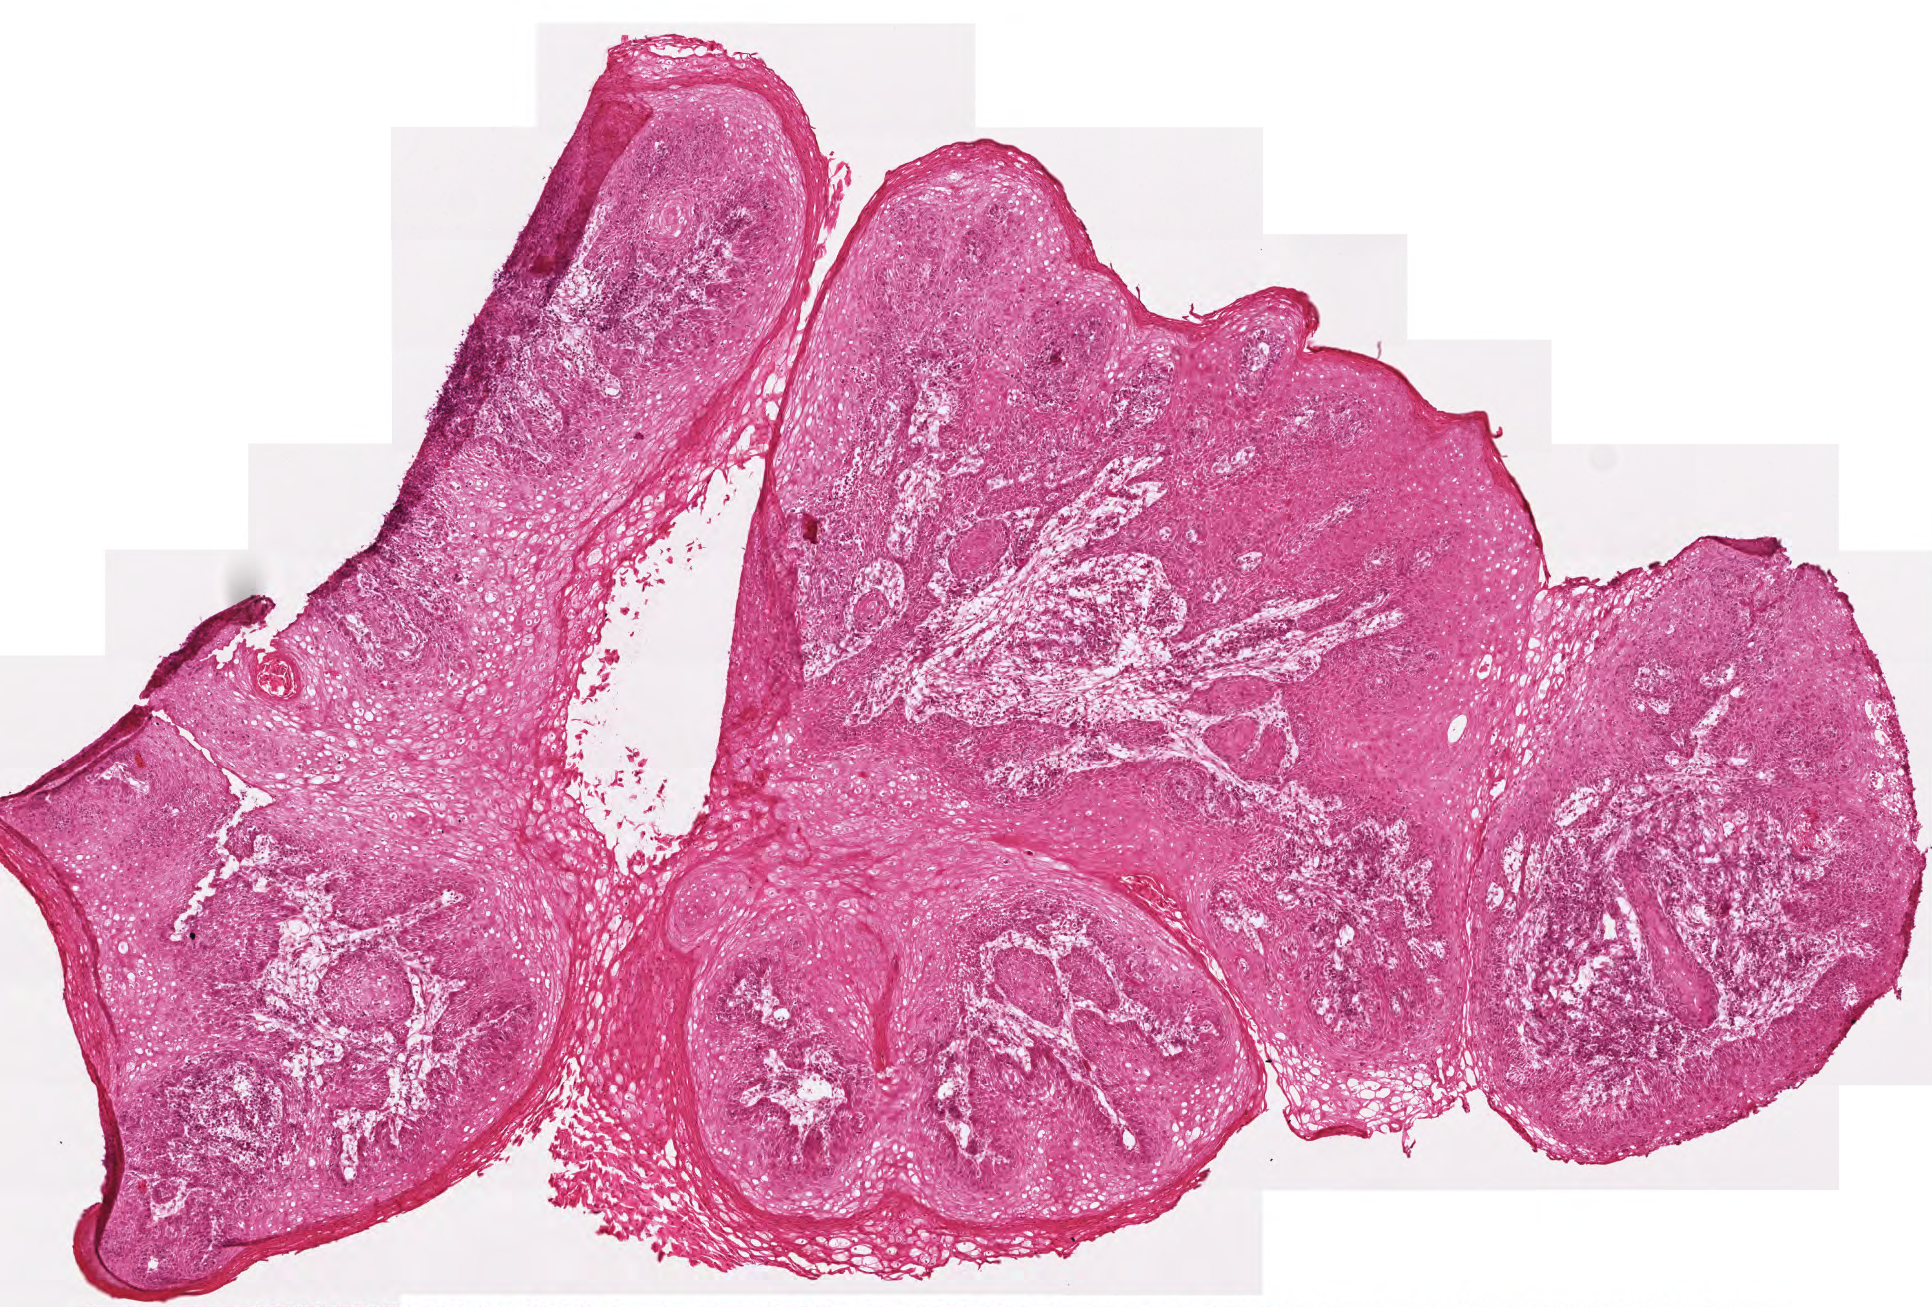
Whole-slide histology image, H&E, shown as a low-resolution overview of the whole scanned area (about 3.9 x 2.6 mm); frozen section from the top of the tissue portion; sample: primary tumour, head and neck. Male, age 70 years at initial diagnosis.
Histologic diagnosis: Squamous cell carcinoma, NOS (tongue, NOS).